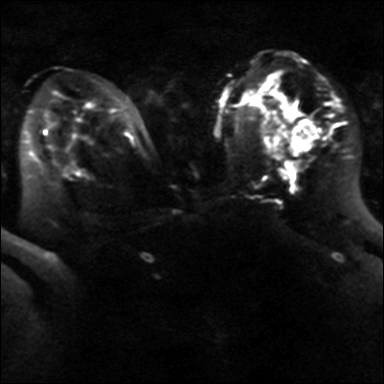
Breast MRI, one axial slice. Position 24 of 40 along the scan axis. Diffusion-weighted series; image 2 of 4 stored at this slice position (different b-values; order by instance number). 3 T. 384 × 384 image matrix, field of view 320 × 320 mm. Female patient.
Annotated regions visible in this slice (expert manual segmentation):
- tumour on diffusion-weighted imaging: bounding box (x1, y1, x2, y2) in pixels: (291, 123, 317, 155)